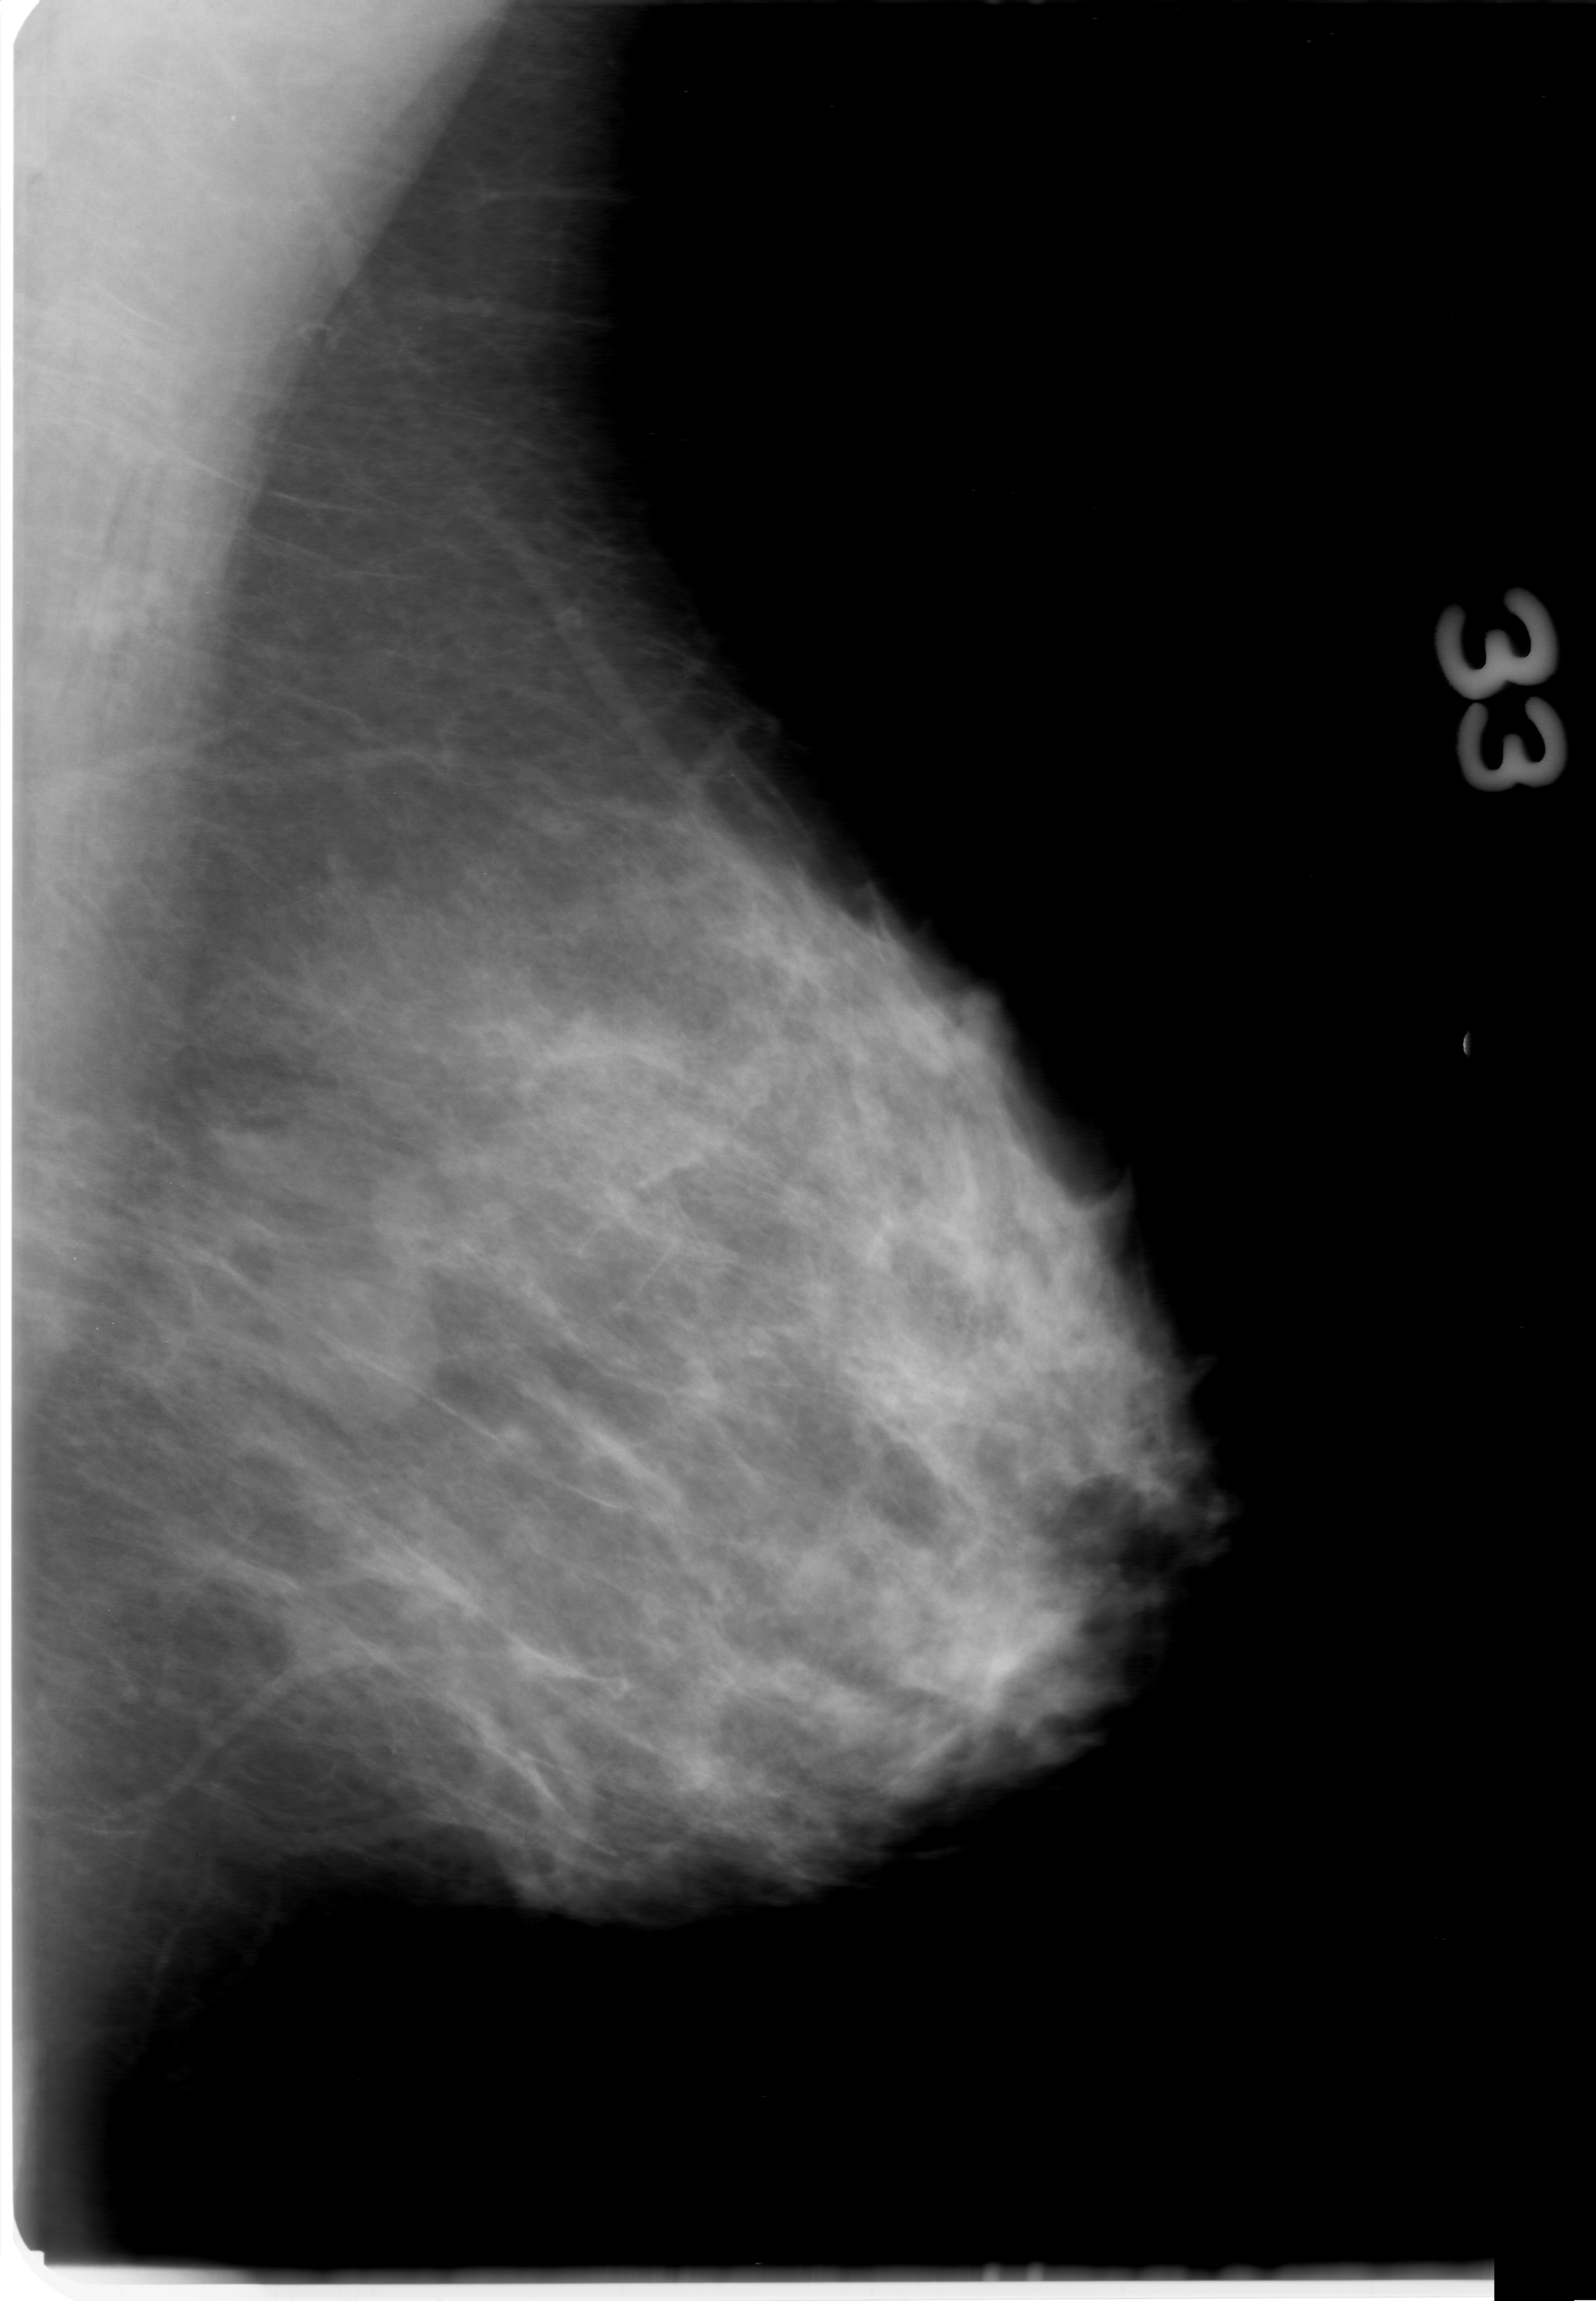
Mammogram (digitized film), left breast, mediolateral oblique (MLO) view, BI-RADS breast density category 3 (scale 1–4).
Marked abnormality: mass, shape oval, margins obscured; BI-RADS assessment category 0; pathology (as recorded): benign.